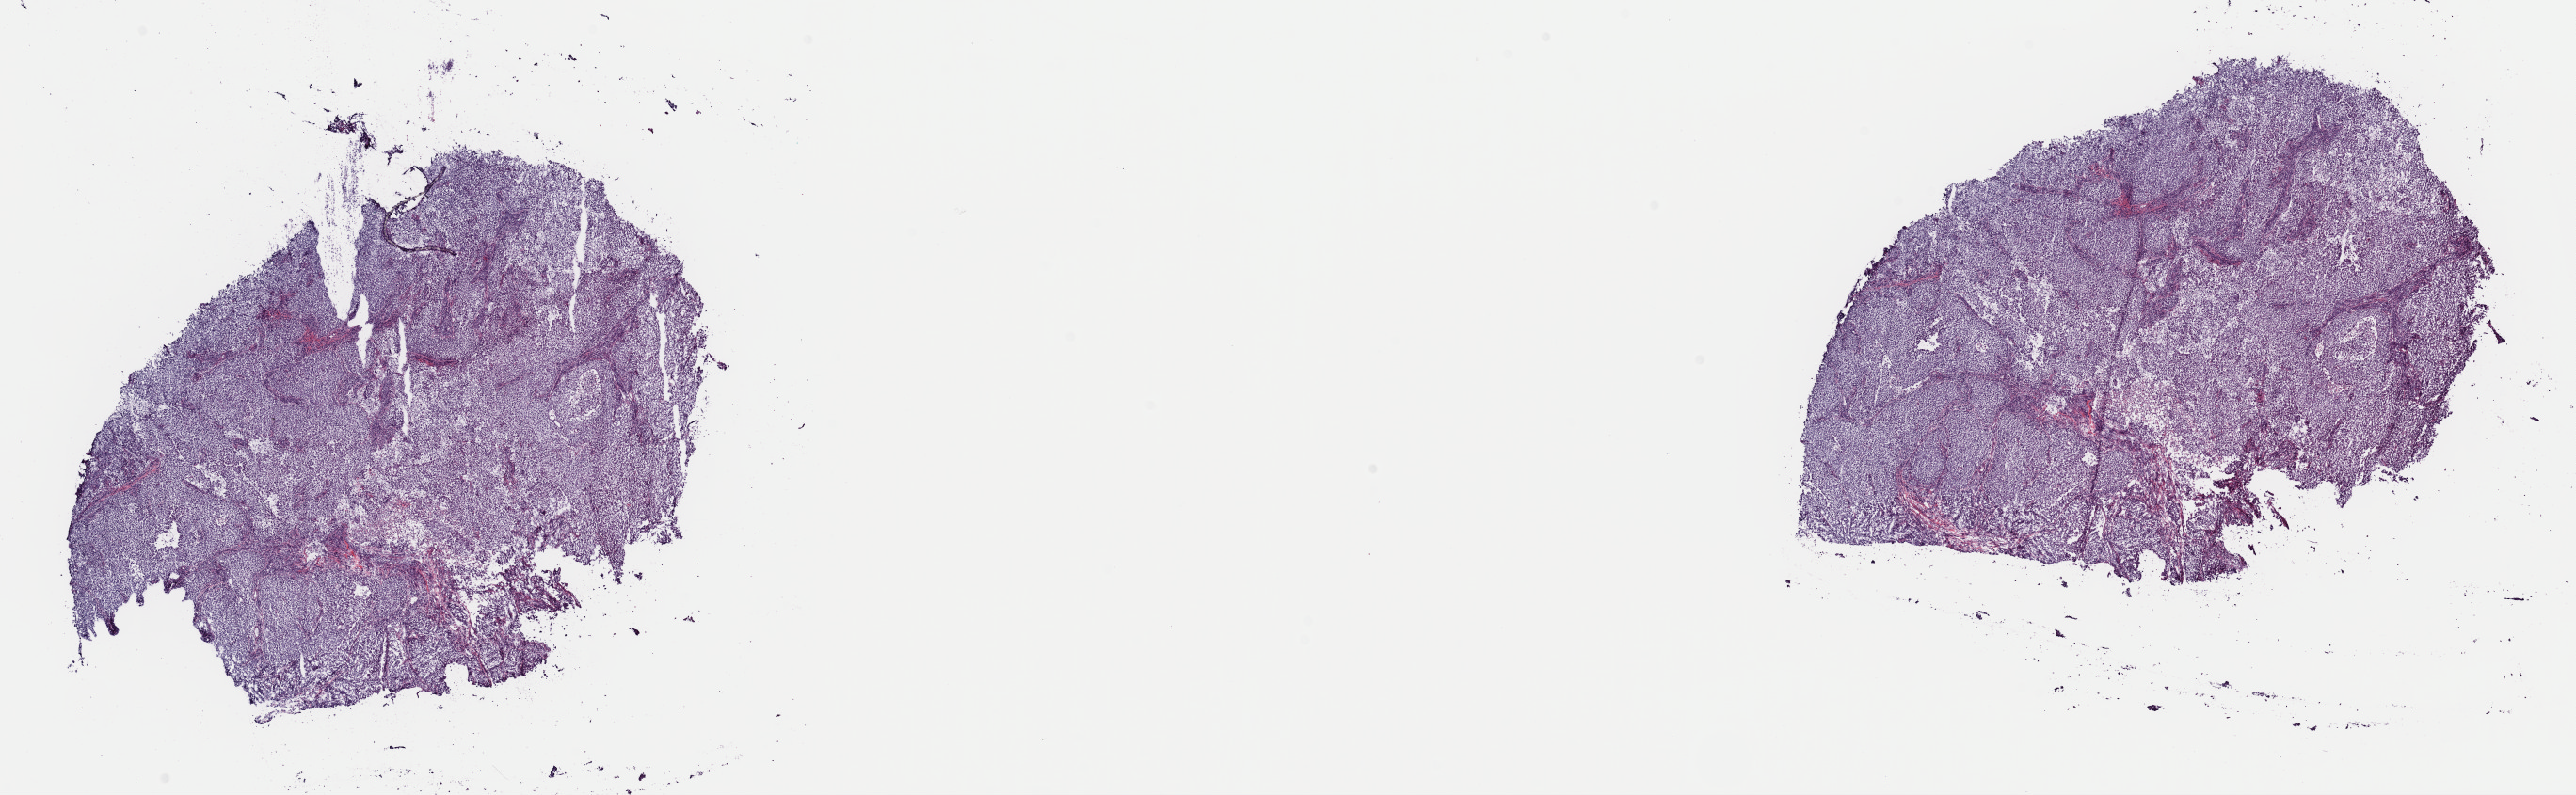
Whole-slide histology image, H&E-stained, low-resolution overview of the scanned area, about 21.6 x 6.7 mm (slide scanned at 40x), frozen section, sample: primary tumour, cervix. Patient: female, age at initial diagnosis 62 years. Histologic grade: G3 (poorly differentiated). Pathologist review of this section (percent, as recorded): tumour cells 99%, tumour nuclei 75%, normal cells 0%, stromal cells 0%, necrosis 1%. Inflammatory infiltration, as recorded: lymphocyte infiltration 5%, monocyte infiltration 0%, neutrophil infiltration 1%.
FIGO stage: IB2. Lymph nodes positive (case pathology): 0 of 11 examined. Pathologic diagnosis: Squamous cell carcinoma, large cell, nonkeratinizing, NOS (cervix uteri).